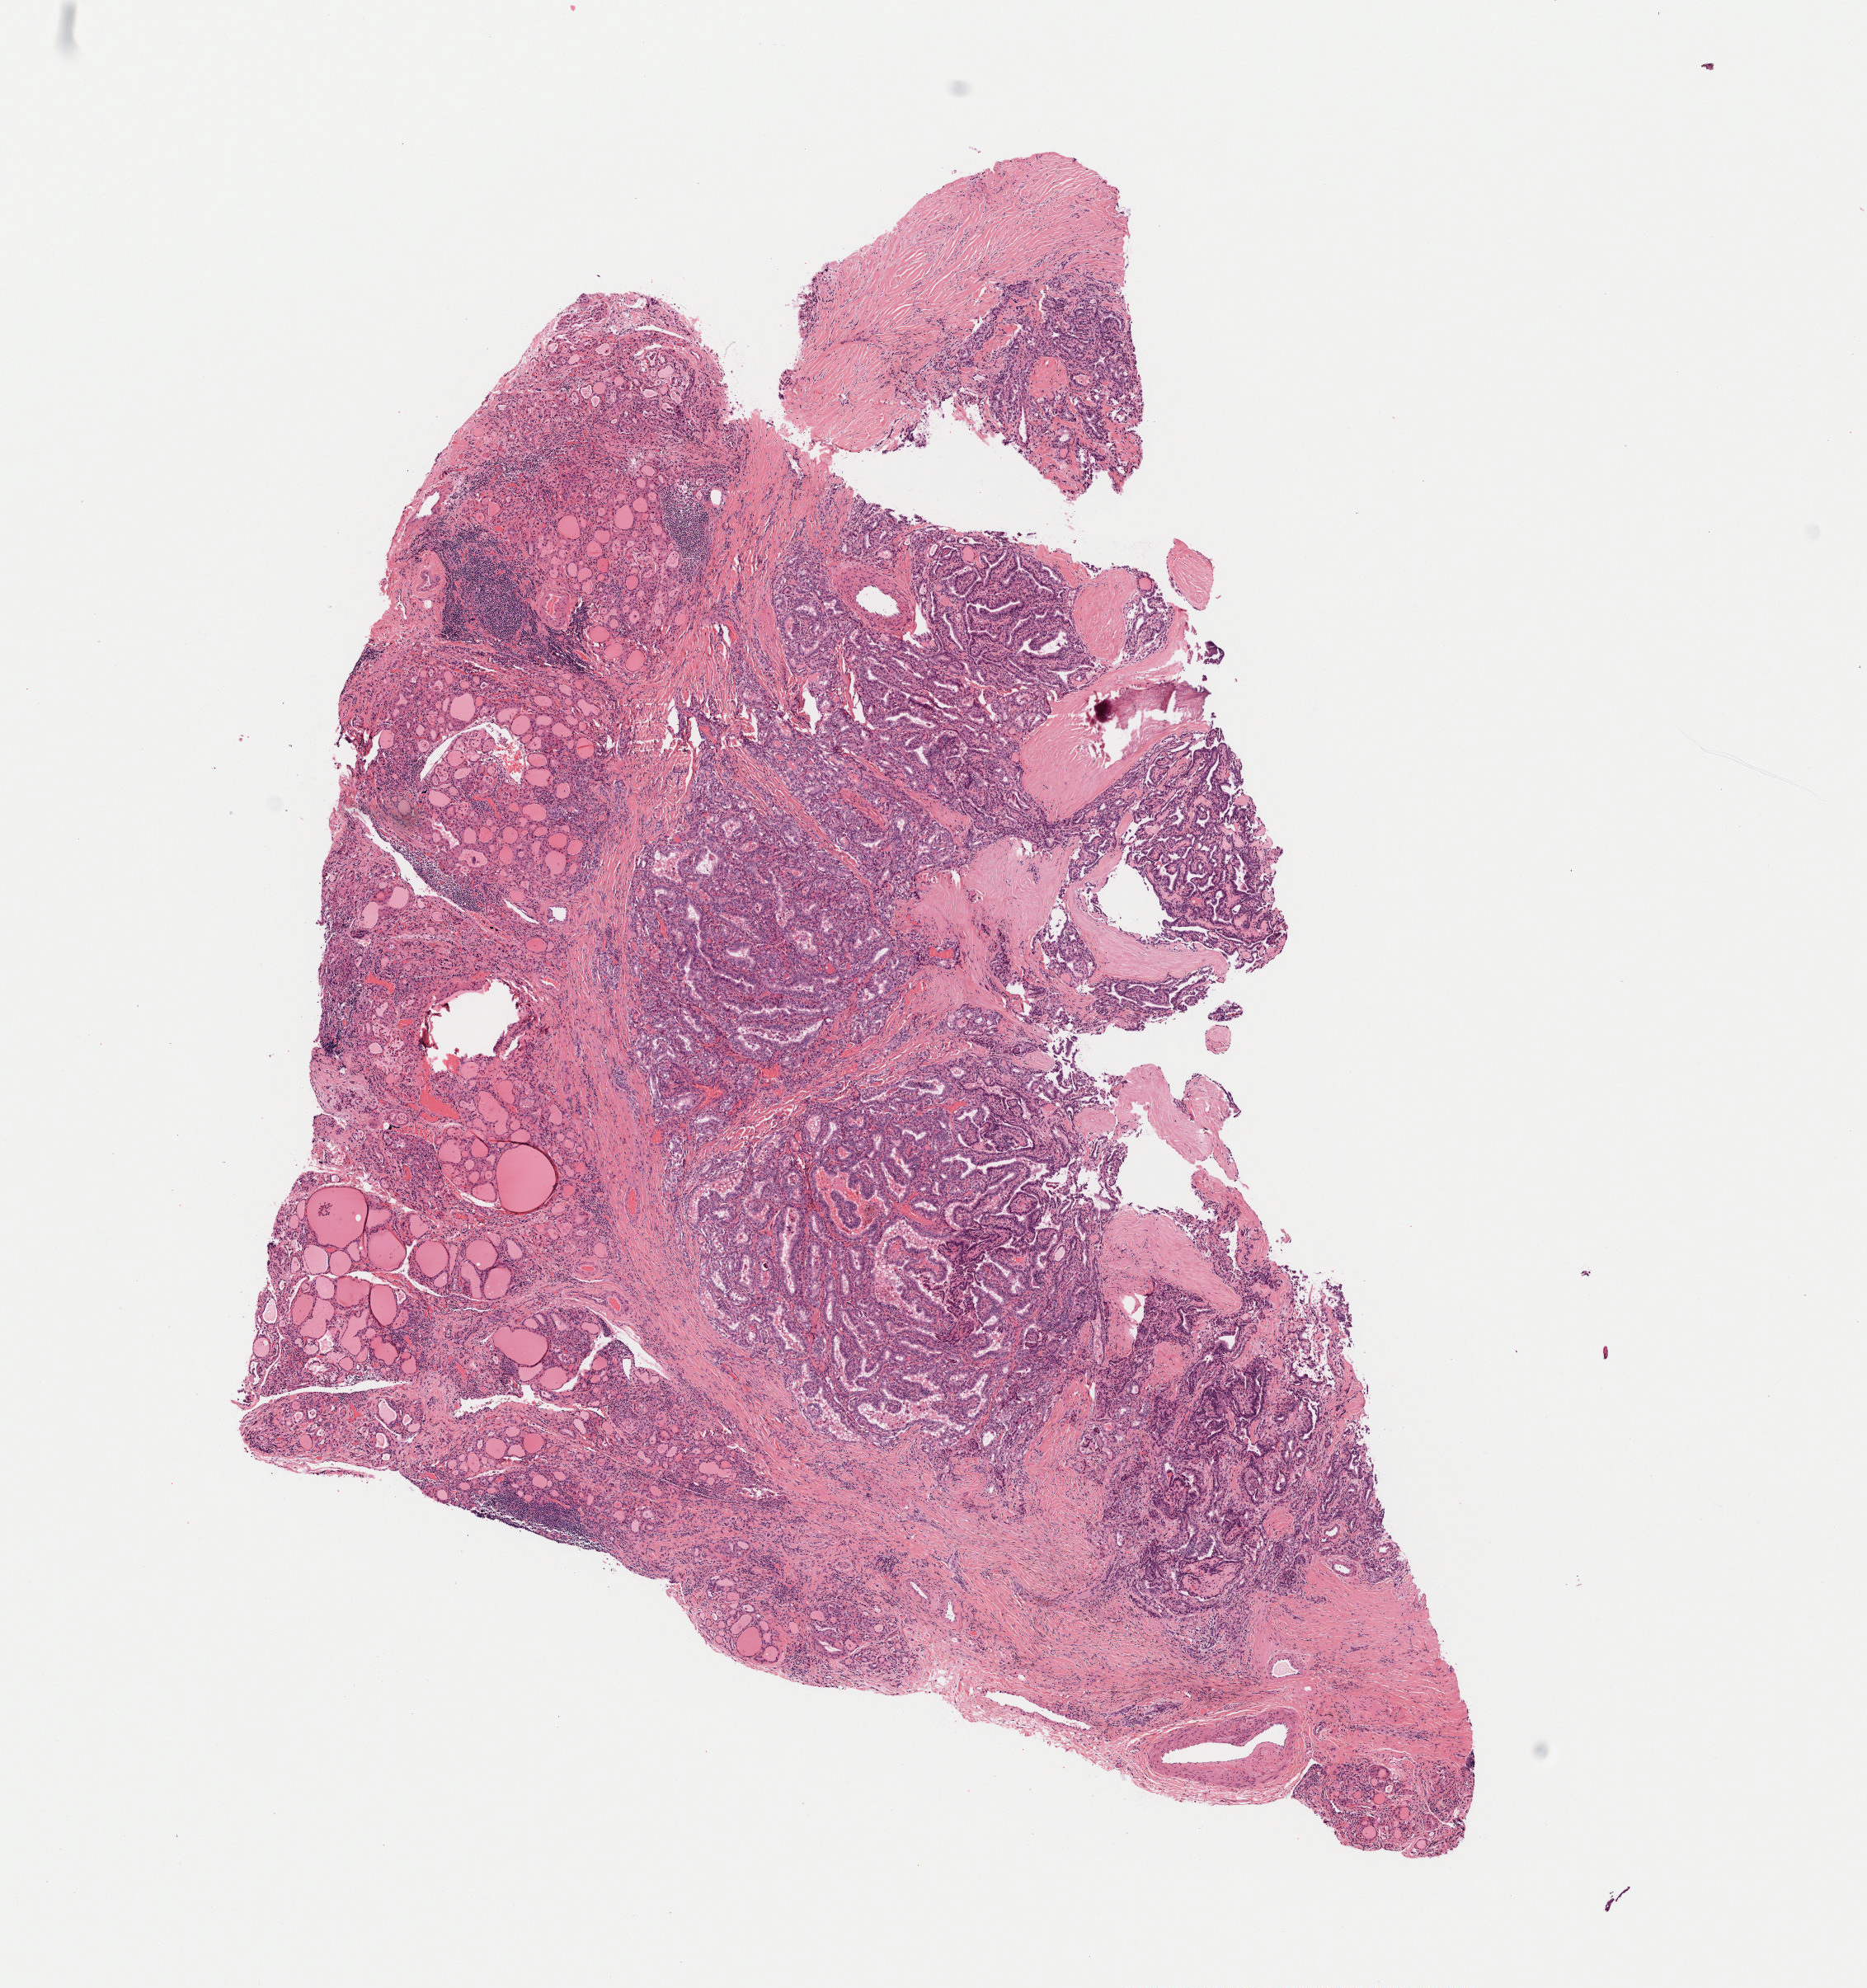
Whole-slide histology image, H&E-stained — whole scanned area (about 9.1 x 9.7 mm, from a 40x scan) shown as a low-resolution overview, formalin-fixed paraffin-embedded (FFPE) diagnostic section, primary tumour sample from the thyroid. Male patient; age at initial diagnosis 72 years.
Histologic diagnosis: Papillary adenocarcinoma, NOS (thyroid gland).